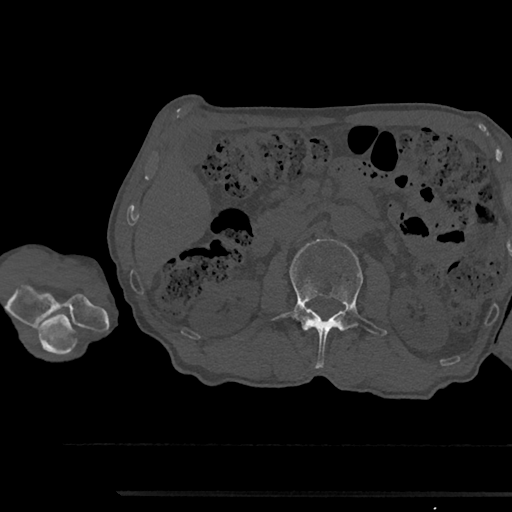
CT including the spine, one axial slice; position 567 of 797 along the scan axis; reconstruction kernel Br40s/3; bone window (W 1800 / L 400 HU); 0.5 mm slice thickness; 512 × 512 image matrix. Male patient, age 79 years. Case-level facts recorded for this patient, not image findings: primary cancer: prostate.
Annotated regions visible in this slice (semi-automatic segmentation, software-assisted and operator-edited):
- L2 vertebra: box from (x=271, y=239) to (x=387, y=368) px